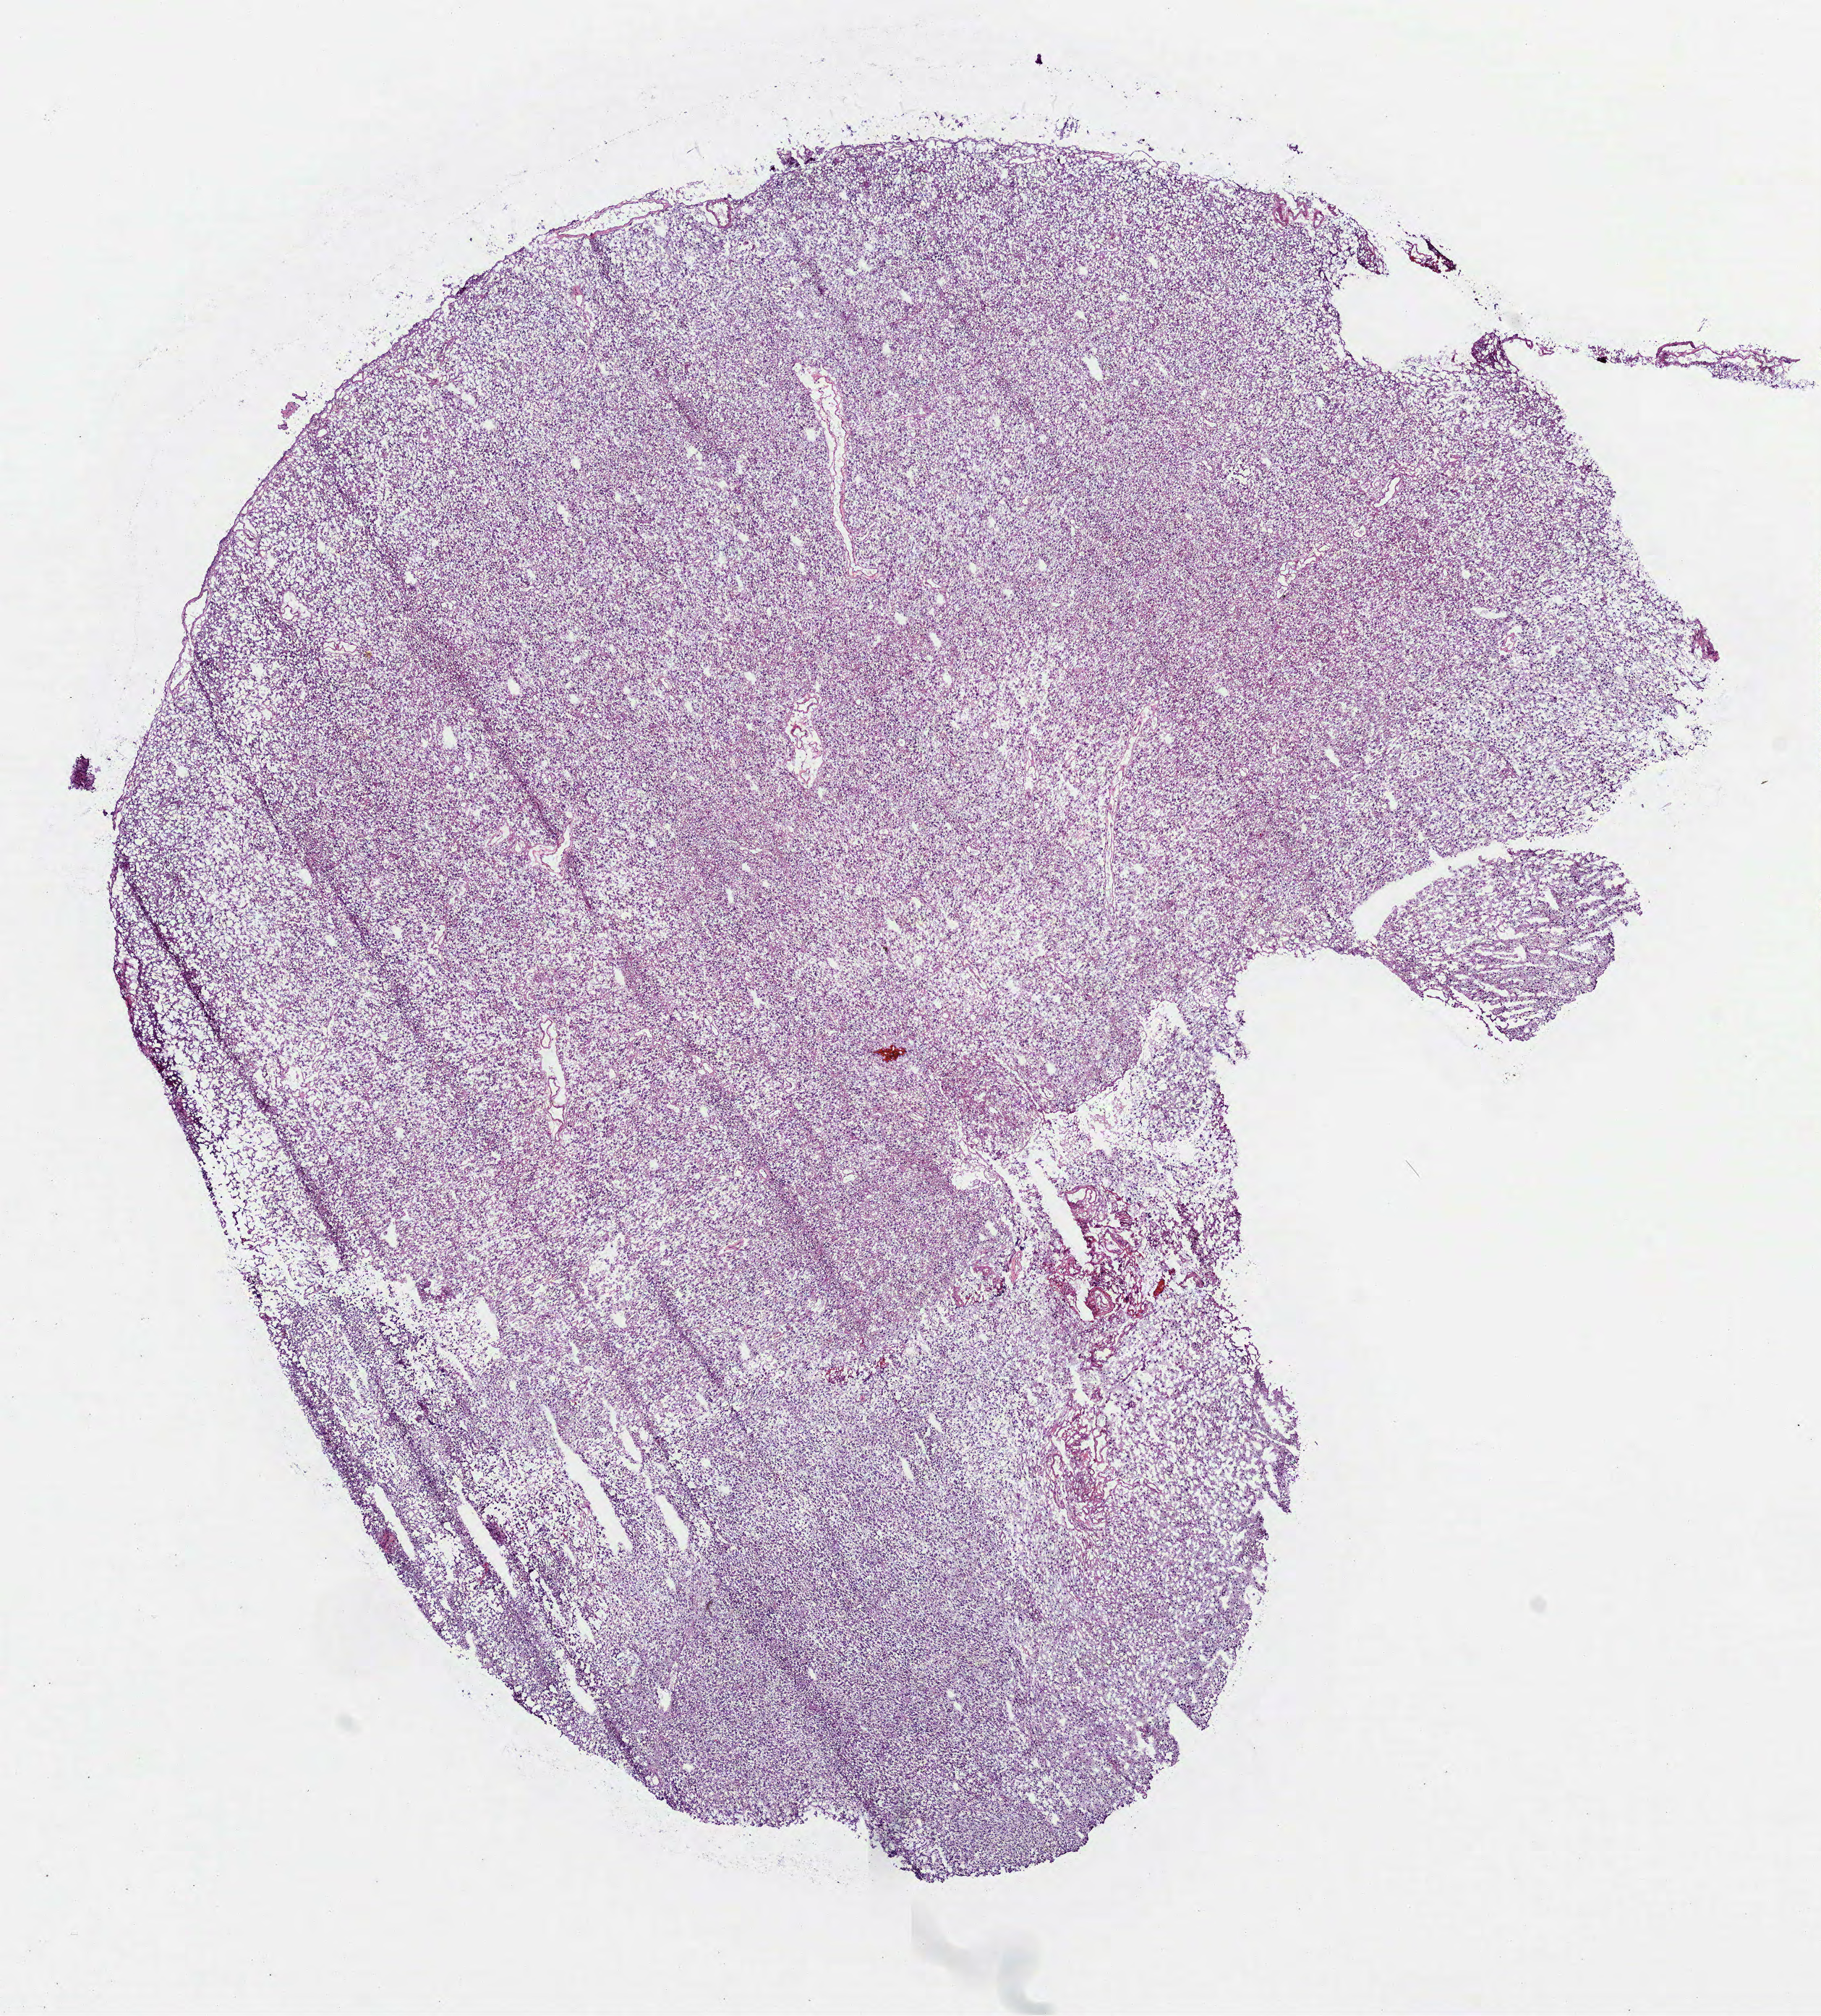
Hematoxylin and eosin (H&E) stained whole-slide image, shown as a low-resolution overview of the whole scanned area (about 10.2 x 11.2 mm). Frozen section. Primary tumour sample from the brain. Female patient; age at initial diagnosis 57 years. Histologic grade: G3 (poorly differentiated). Slide review estimates, as recorded: tumour cells 100%, tumour nuclei 80%, normal cells 0%, stromal cells 0%, necrosis 0%.
* pathologic diagnosis: Oligodendroglioma, anaplastic (cerebrum)